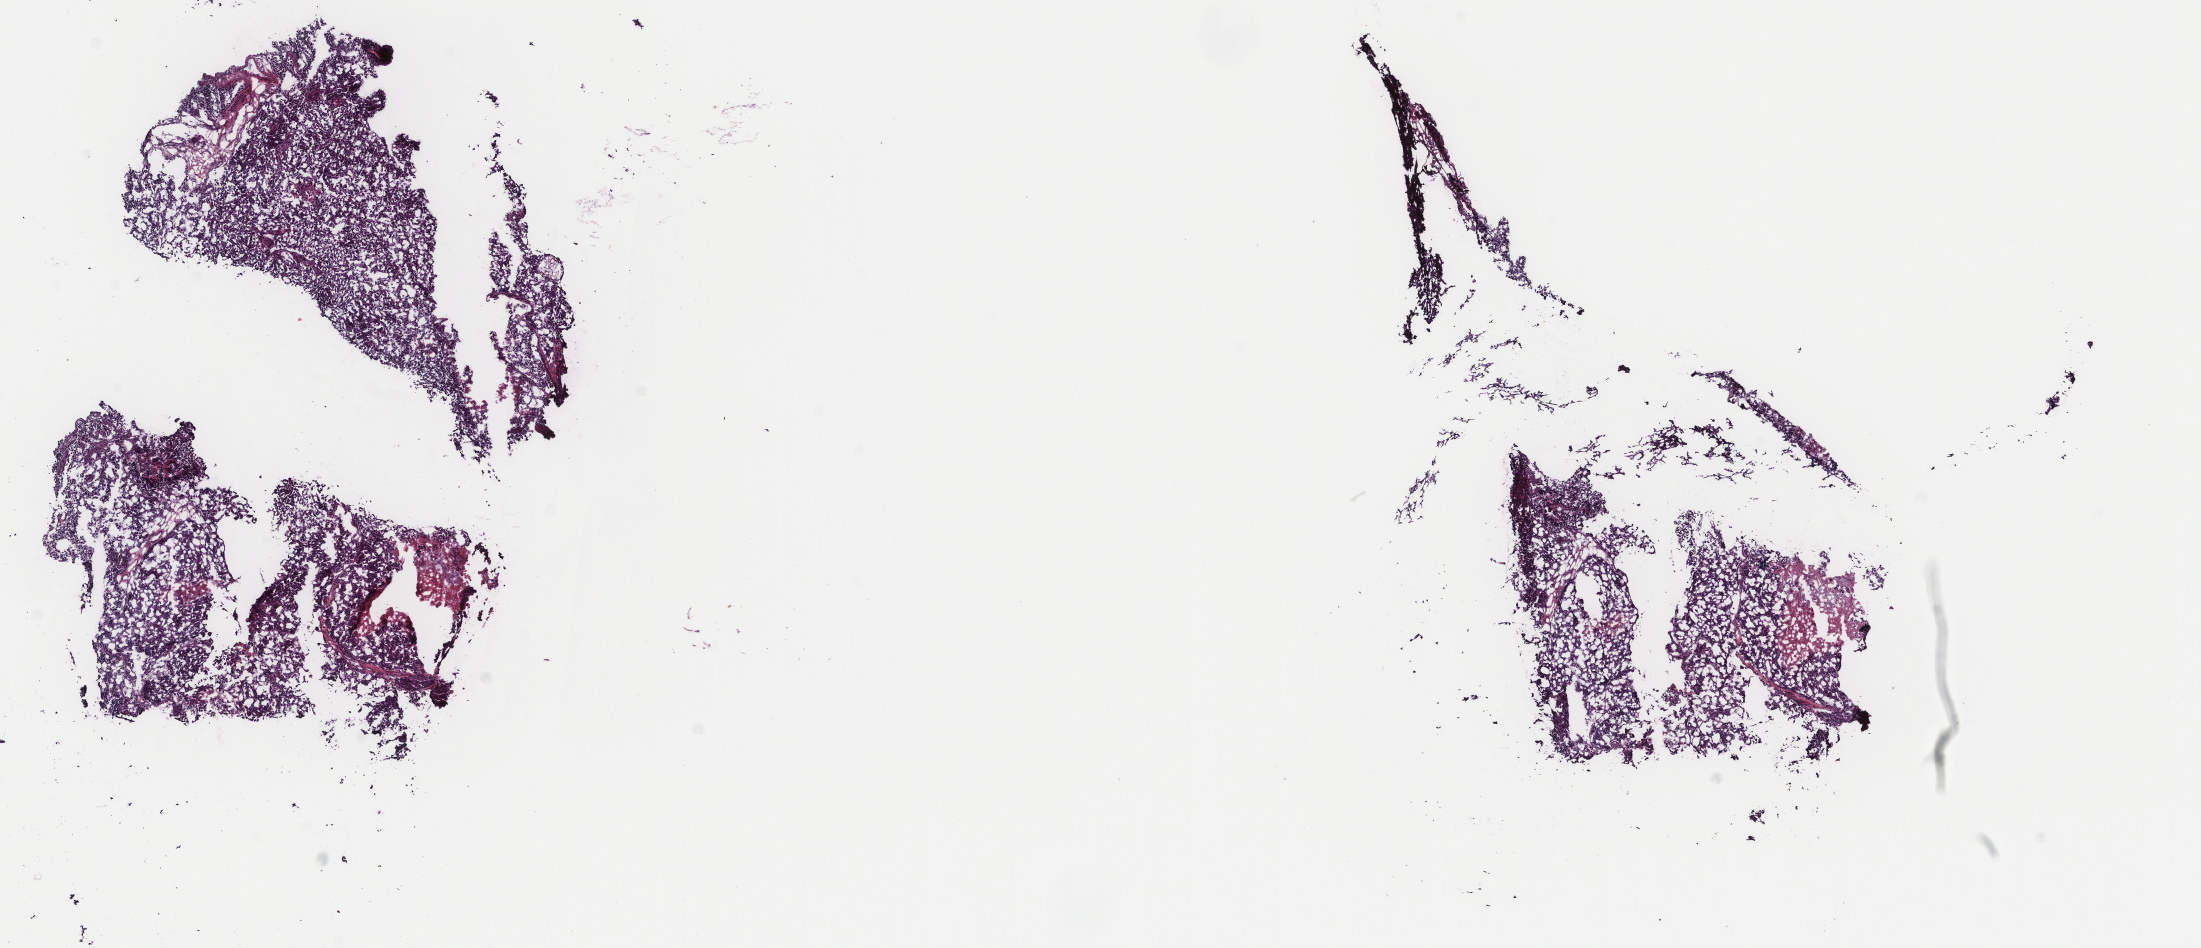
Digitized H&E tissue section (whole slide), low-resolution overview of the scanned area, about 17.5 x 7.5 mm (slide scanned at 40x), frozen section from the top of the tissue portion, primary tumour sample from the bladder. Patient: female, age at initial diagnosis 80 years. Histologic grade: high grade. Composition of this section per pathologist review: tumour cells 75%, tumour nuclei 80%, normal cells 0%, stromal cells 20%, necrosis 5%. Inflammatory infiltration, as recorded: lymphocyte infiltration 2%, monocyte infiltration 0%, neutrophil infiltration 0%.
* TNM: T2 N0 MX
* diagnosis: Transitional cell carcinoma
* lymph nodes positive (case pathology): 0 of 2 examined
* AJCC pathologic stage: II (7th edition)